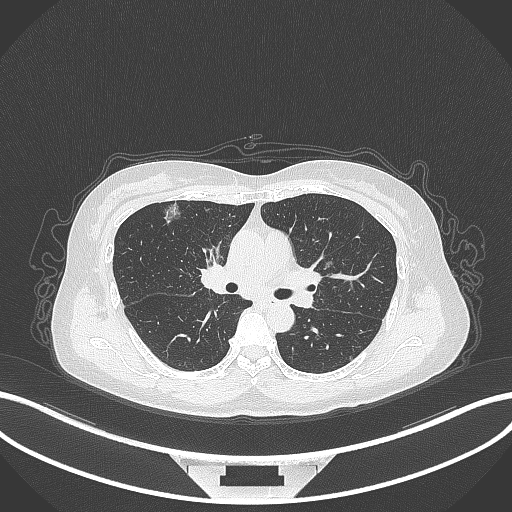
Chest CT, one axial slice. Position 197 of 315 along the scan axis. Reconstruction kernel B70f. 120 kVp. Lung window (W 1500 / L -600 HU). 1 mm slice thickness. 512 × 512 image matrix, field of view 400 × 400 mm. Female patient, age 61 years. From the clinical record (not read from this slice): clinical TNM (as recorded): T1b N0 M0; histopathological grade: G1.
Outlined on this slice (rectangle marked by the reading radiologist):
- lung tumour (recorded histology: adenocarcinoma): bounding box (x1, y1, x2, y2) in pixels: (158, 199, 183, 228)